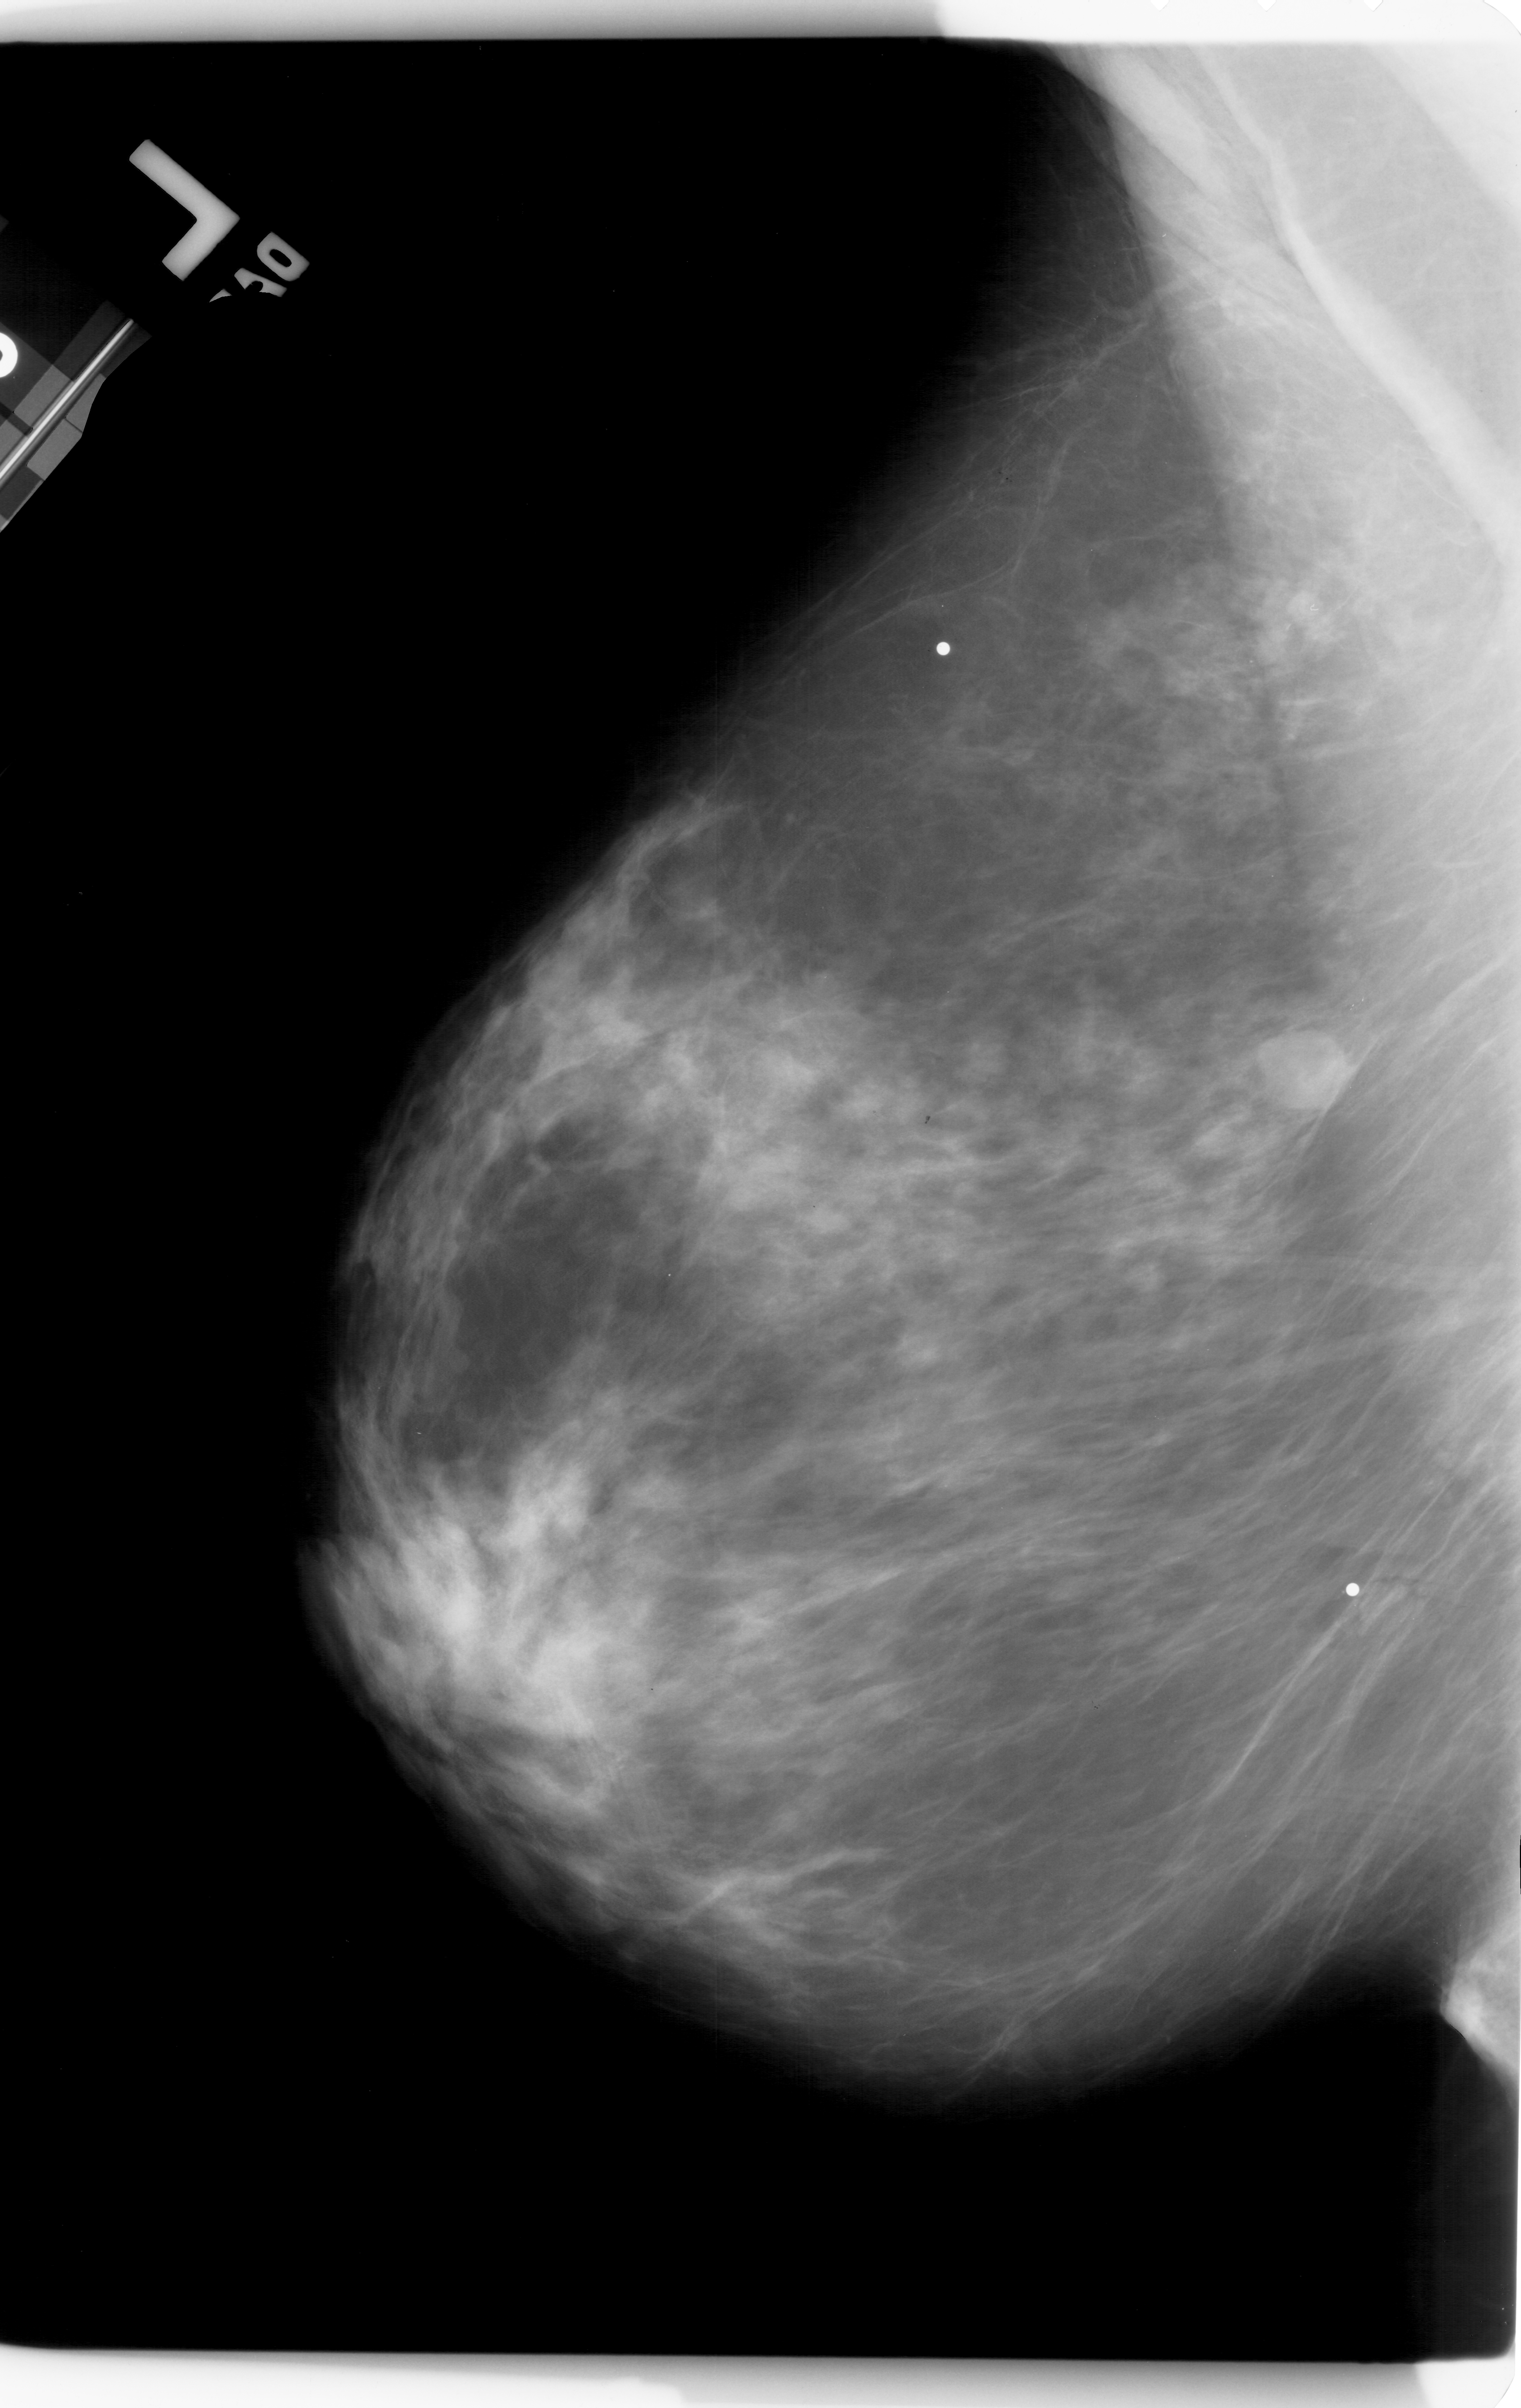
Scanned film-screen mammogram. Left breast. Mediolateral oblique (MLO) view. Breast composition: heterogeneously dense (BI-RADS density category 3 of 4). 1521 × 2408 image matrix.
Expert-marked regions of interest on this film, with their recorded descriptors:
- mass, shape lobulated, margins obscured; BI-RADS assessment category 4; pathology result (as recorded, not read from the image): malignant: bounding box [x1, y1, x2, y2] px = [1263, 1040, 1360, 1122]